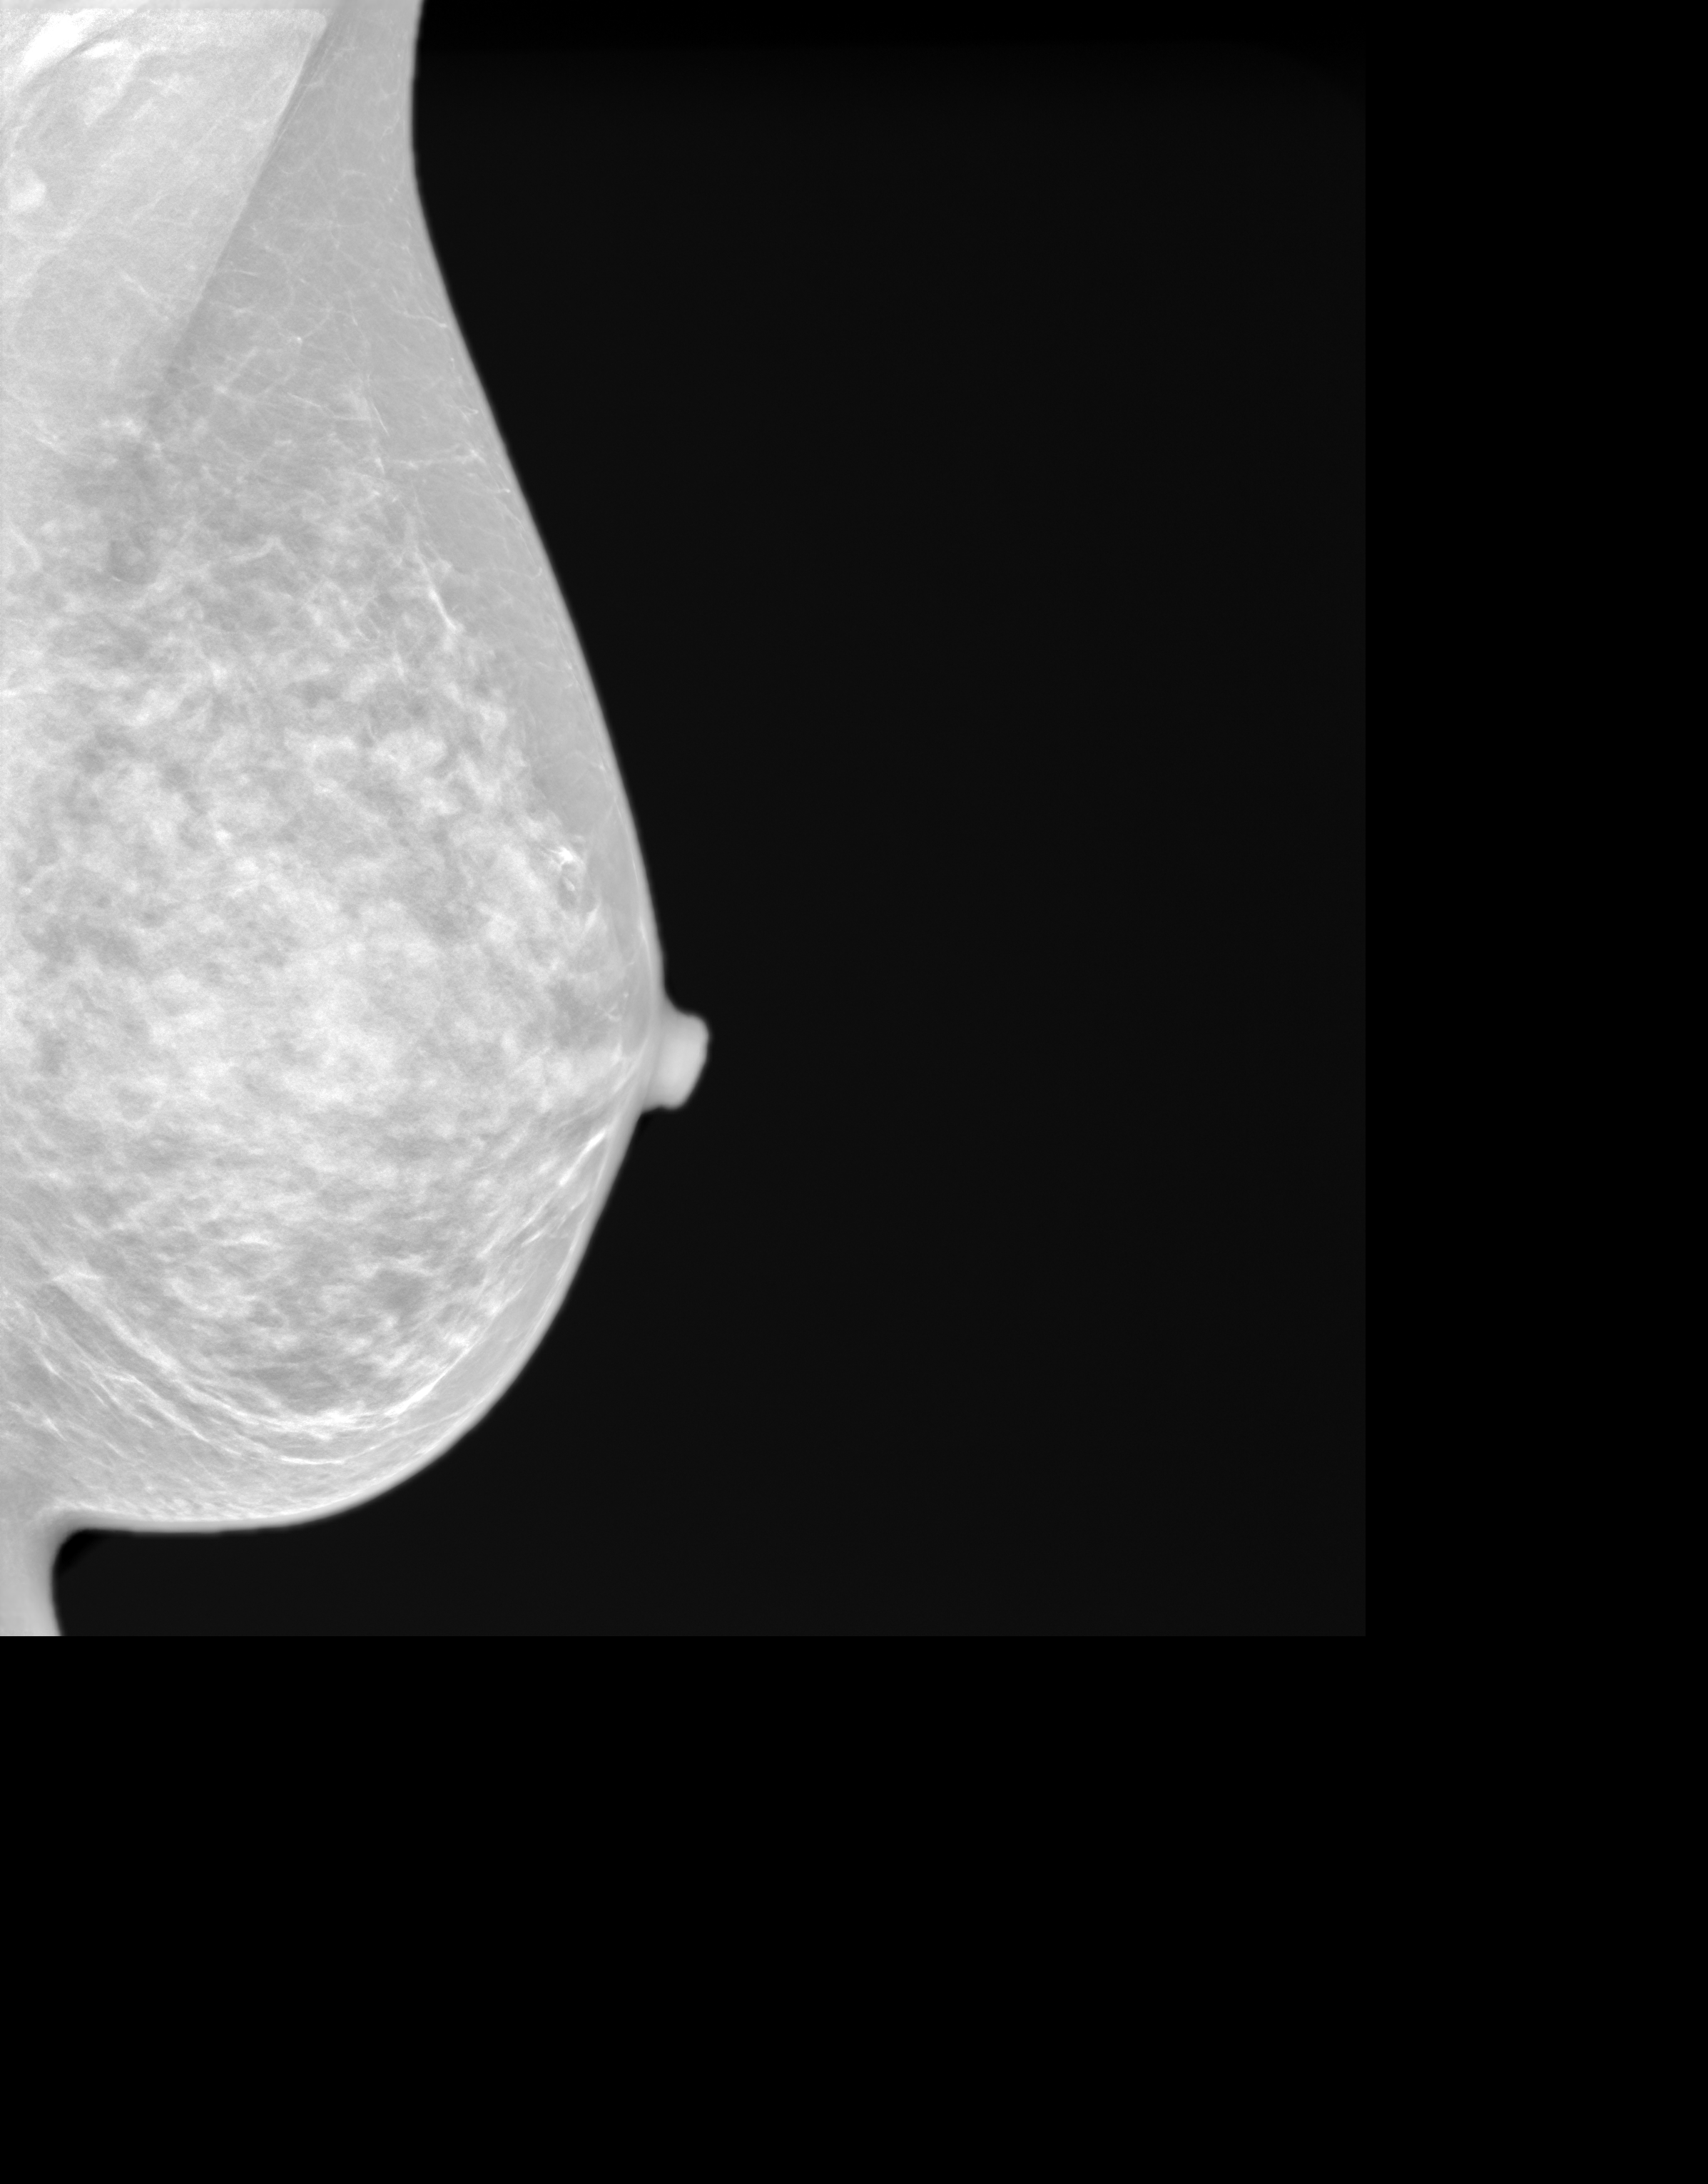
Synthesized 2-D mammogram reconstructed from digital breast tomosynthesis, left breast, mediolateral oblique (MLO) view, screening examination. Patient aged 60 years (female).
- breast density at the screening exam (both breasts): extremely dense (BI-RADS density category d)
- final BI-RADS category for the screening round (tomosynthesis exam, both breasts): category 1
- recall: no recall after this screen